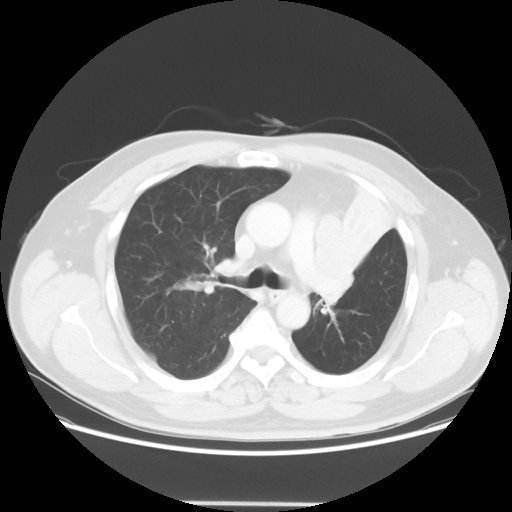
Chest CT, one axial slice; position 40 of 62 along the scan axis; reconstruction kernel STANDARD; lung window (W 1500 / L -600 HU); 5 mm slice thickness; 512 × 512 image matrix, field of view 403 × 403 mm. Male patient, age 49 years. From the clinical record (not read from this slice): clinical TNM (as recorded): T3 N3 M1c.
Outlined on this slice (rectangle marked by the reading radiologist):
- lung tumour (recorded histology: squamous cell carcinoma): box from (x=301, y=210) to (x=366, y=317) px